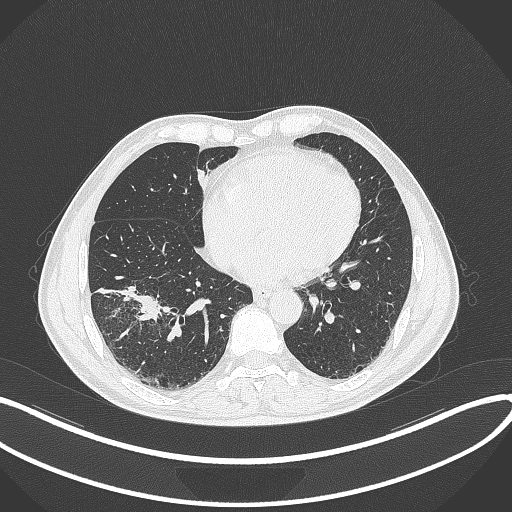
Chest CT, one axial slice; position 130 of 364 along the scan axis; reconstruction kernel B70f; 120 kVp; lung window (W 1500 / L -600 HU); 512 × 512 image matrix. Patient: male, 58 years. Case-level facts recorded for this patient, not image findings: clinical TNM (as recorded): T3 N0 M0; histopathological grade: G2.
Annotated regions visible in this slice (bounding box drawn by a radiologist):
- lung tumour (recorded histology: squamous cell carcinoma): bounding box <137,293,165,328> (left, top, right, bottom; pixels)